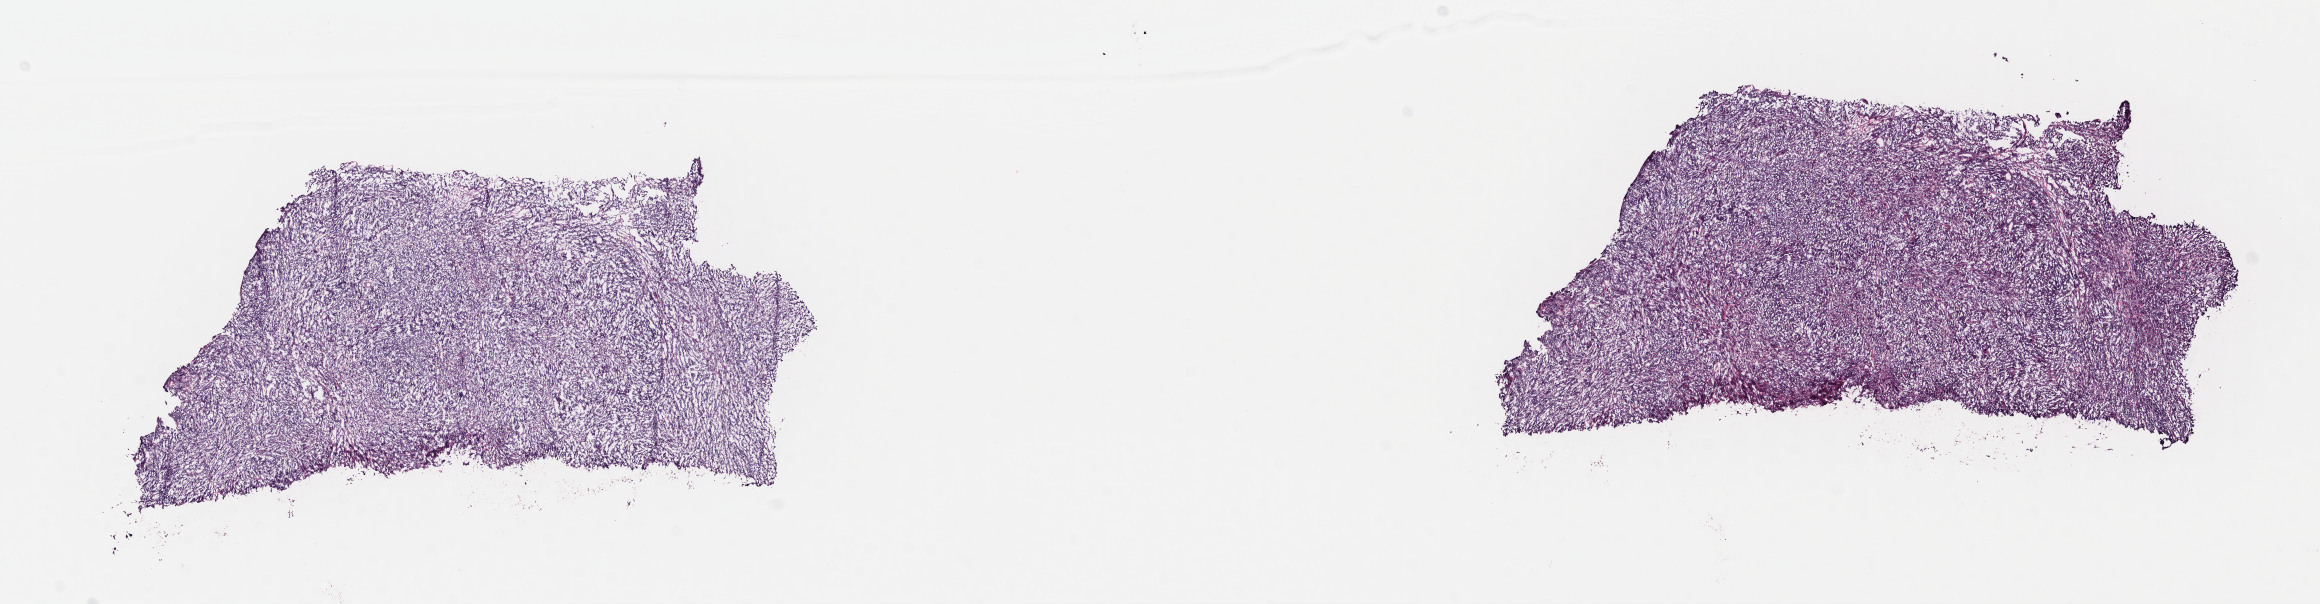
Hematoxylin and eosin (H&E) stained whole-slide image, low-resolution overview of the scanned area, about 18.2 x 4.7 mm; frozen section from the top of the tissue portion; metastatic tumour sample, sampled site: lymph nodes of inguinal region or leg. Patient: female, age at initial diagnosis 18 years. Pathologist review of this section (percent, as recorded): tumour cells 75%, tumour nuclei 75%, normal cells 0%, stromal cells 24%, necrosis 1%. Infiltration values recorded for this section: lymphocyte infiltration 5%, monocyte infiltration 1%, neutrophil infiltration 0%.
This section: metastatic tumour tissue. Patient diagnosis: Malignant melanoma, NOS.